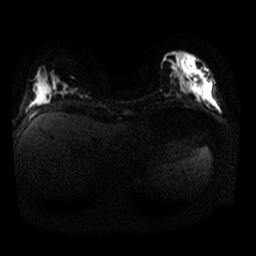
Breast MRI, one axial slice. Position 9 of 25 along the scan axis. Diffusion-weighted series; image 2 of 4 stored at this slice position (different b-values; order by instance number). 1.5 T. 4 mm slice thickness. 256 × 256 image matrix, field of view 320 × 320 mm. Female patient.
Structures marked on this image (expert manual segmentation):
- tumour on diffusion-weighted imaging: bounding box [x1, y1, x2, y2] px = [205, 83, 213, 92]